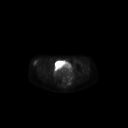
FDG PET of an extremity soft-tissue mass (from a PET/CT study), one axial slice. Slice 72 of 267 in the series (ordered by position). 3.27 mm slice thickness. 128 × 128 image matrix, field of view 700 × 700 mm. Patient: female, 34 years. Case-level facts recorded for this patient, not image findings: histological type: synovial sarcoma; grade: intermediate; site of the primary tumour: right thigh.
Structures marked on this image (expert contour drawn on MRI and transferred to this co-registered scan by the dataset authors):
- gross tumour volume including surrounding oedema: box from (x=33, y=60) to (x=37, y=66) px
- gross tumour volume (mass): (x=33, y=61)–(x=37, y=66)